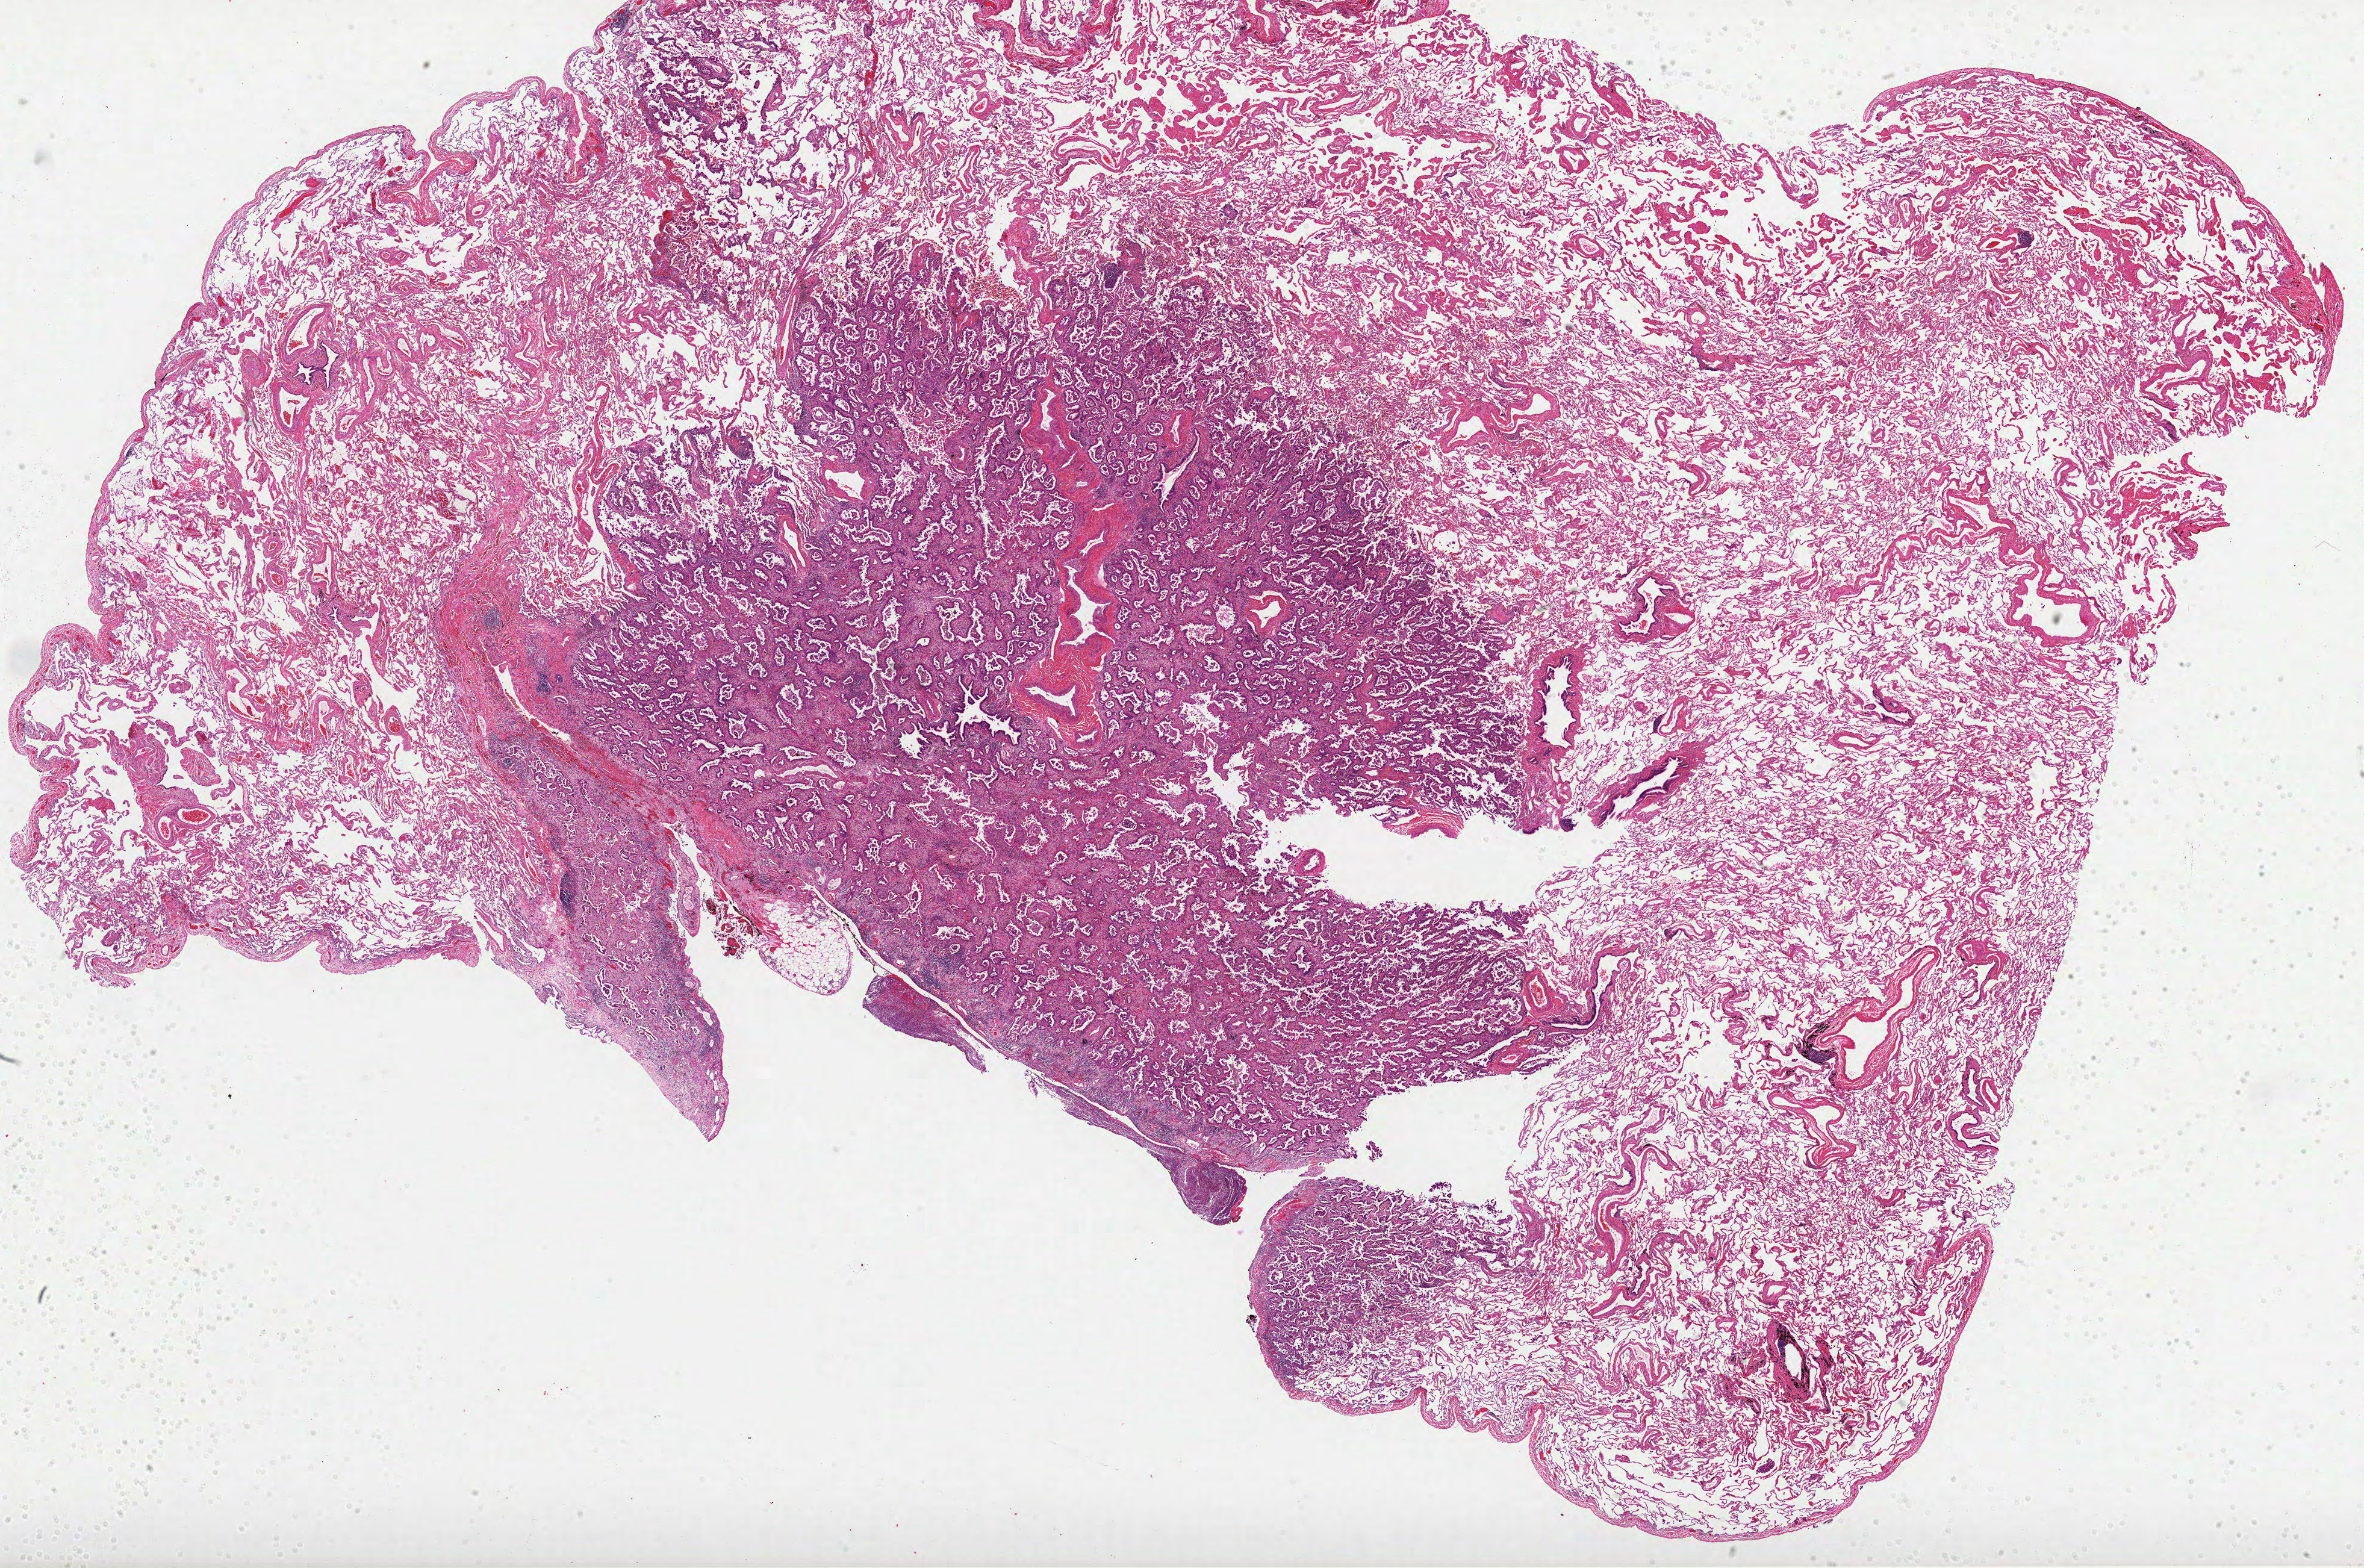
H&E whole-slide image — shown as a low-resolution overview of the whole scanned area (about 31.7 x 21.0 mm); FFPE section; sample: primary tumour, lung. Female patient; age at initial diagnosis 61 years.
AJCC pathologic stage: IIB (4th edition). Pathologic diagnosis: Adenocarcinoma, NOS (lower lobe, lung).